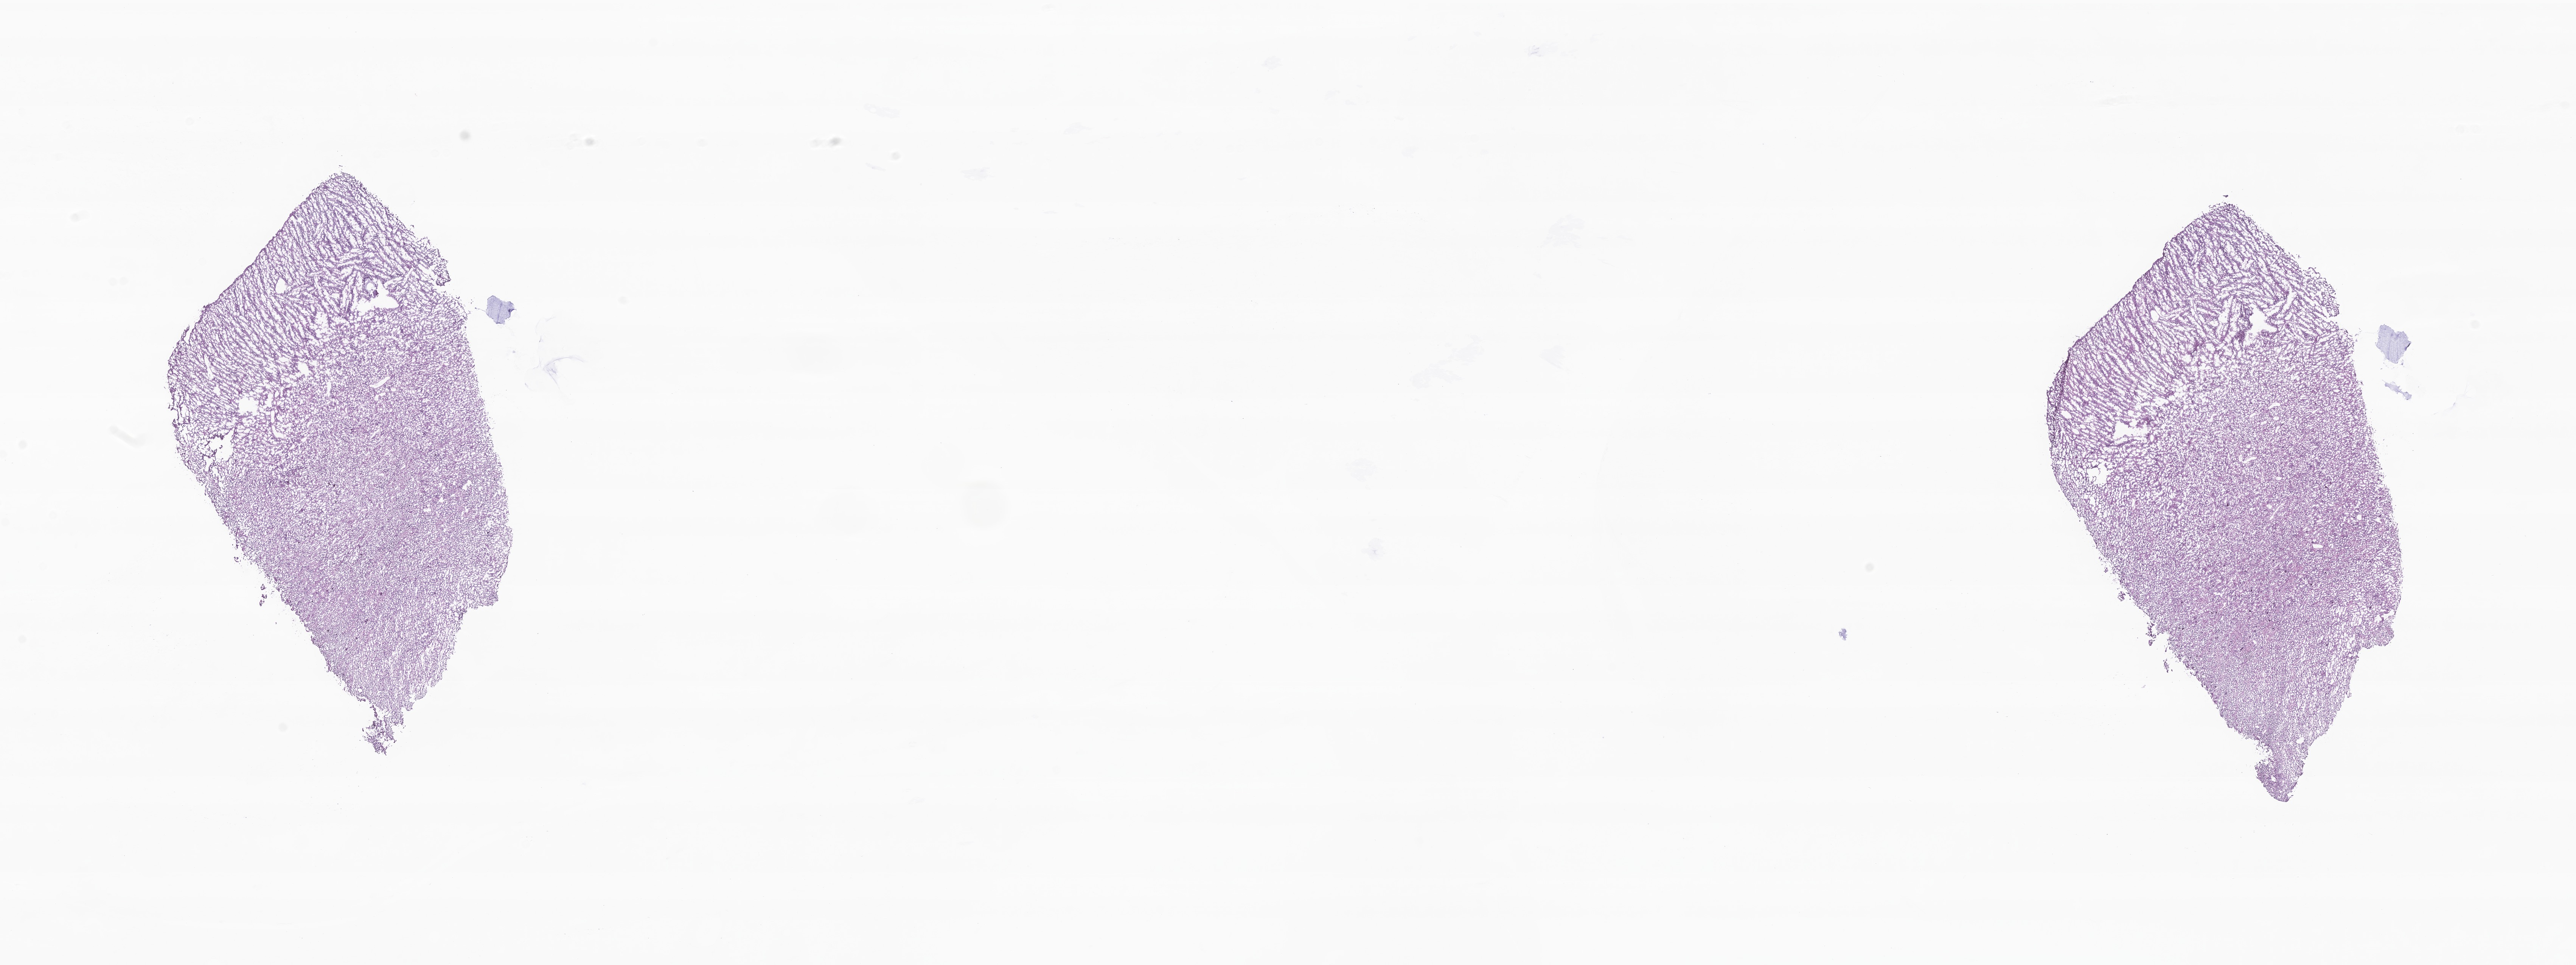
Whole-slide image, haematoxylin and eosin stain of tumor tissue from the brain stem — a low-resolution overview of the entire scanned area, about 28.7 x 10.8 mm; frozen section. Patient female; age 908 days (about 2.5 years).
- recorded diagnosis: Ependymoma, NOS